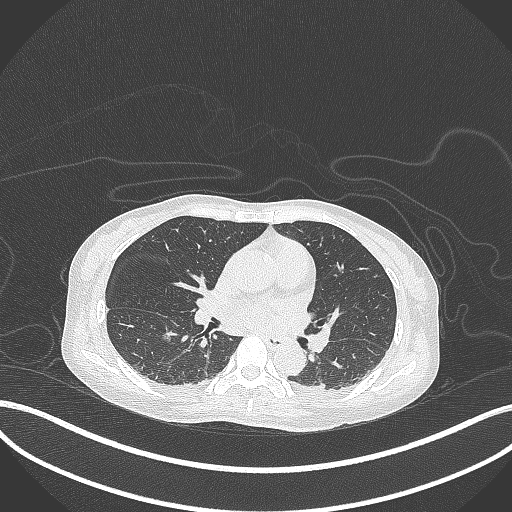
Chest CT, one axial slice; position 160 of 261 along the scan axis; reconstruction kernel B70f; 120 kVp; lung window (W 1500 / L -600 HU); 512 × 512 image matrix, field of view 400 × 400 mm. Patient: female, 44 years. Case-level facts recorded for this patient, not image findings: clinical TNM (as recorded): T1c N0 M0.
Annotated regions visible in this slice (rectangle marked by the reading radiologist):
- lung tumour (recorded histology: adenocarcinoma): bounding box <158,329,176,343> (left, top, right, bottom; pixels)